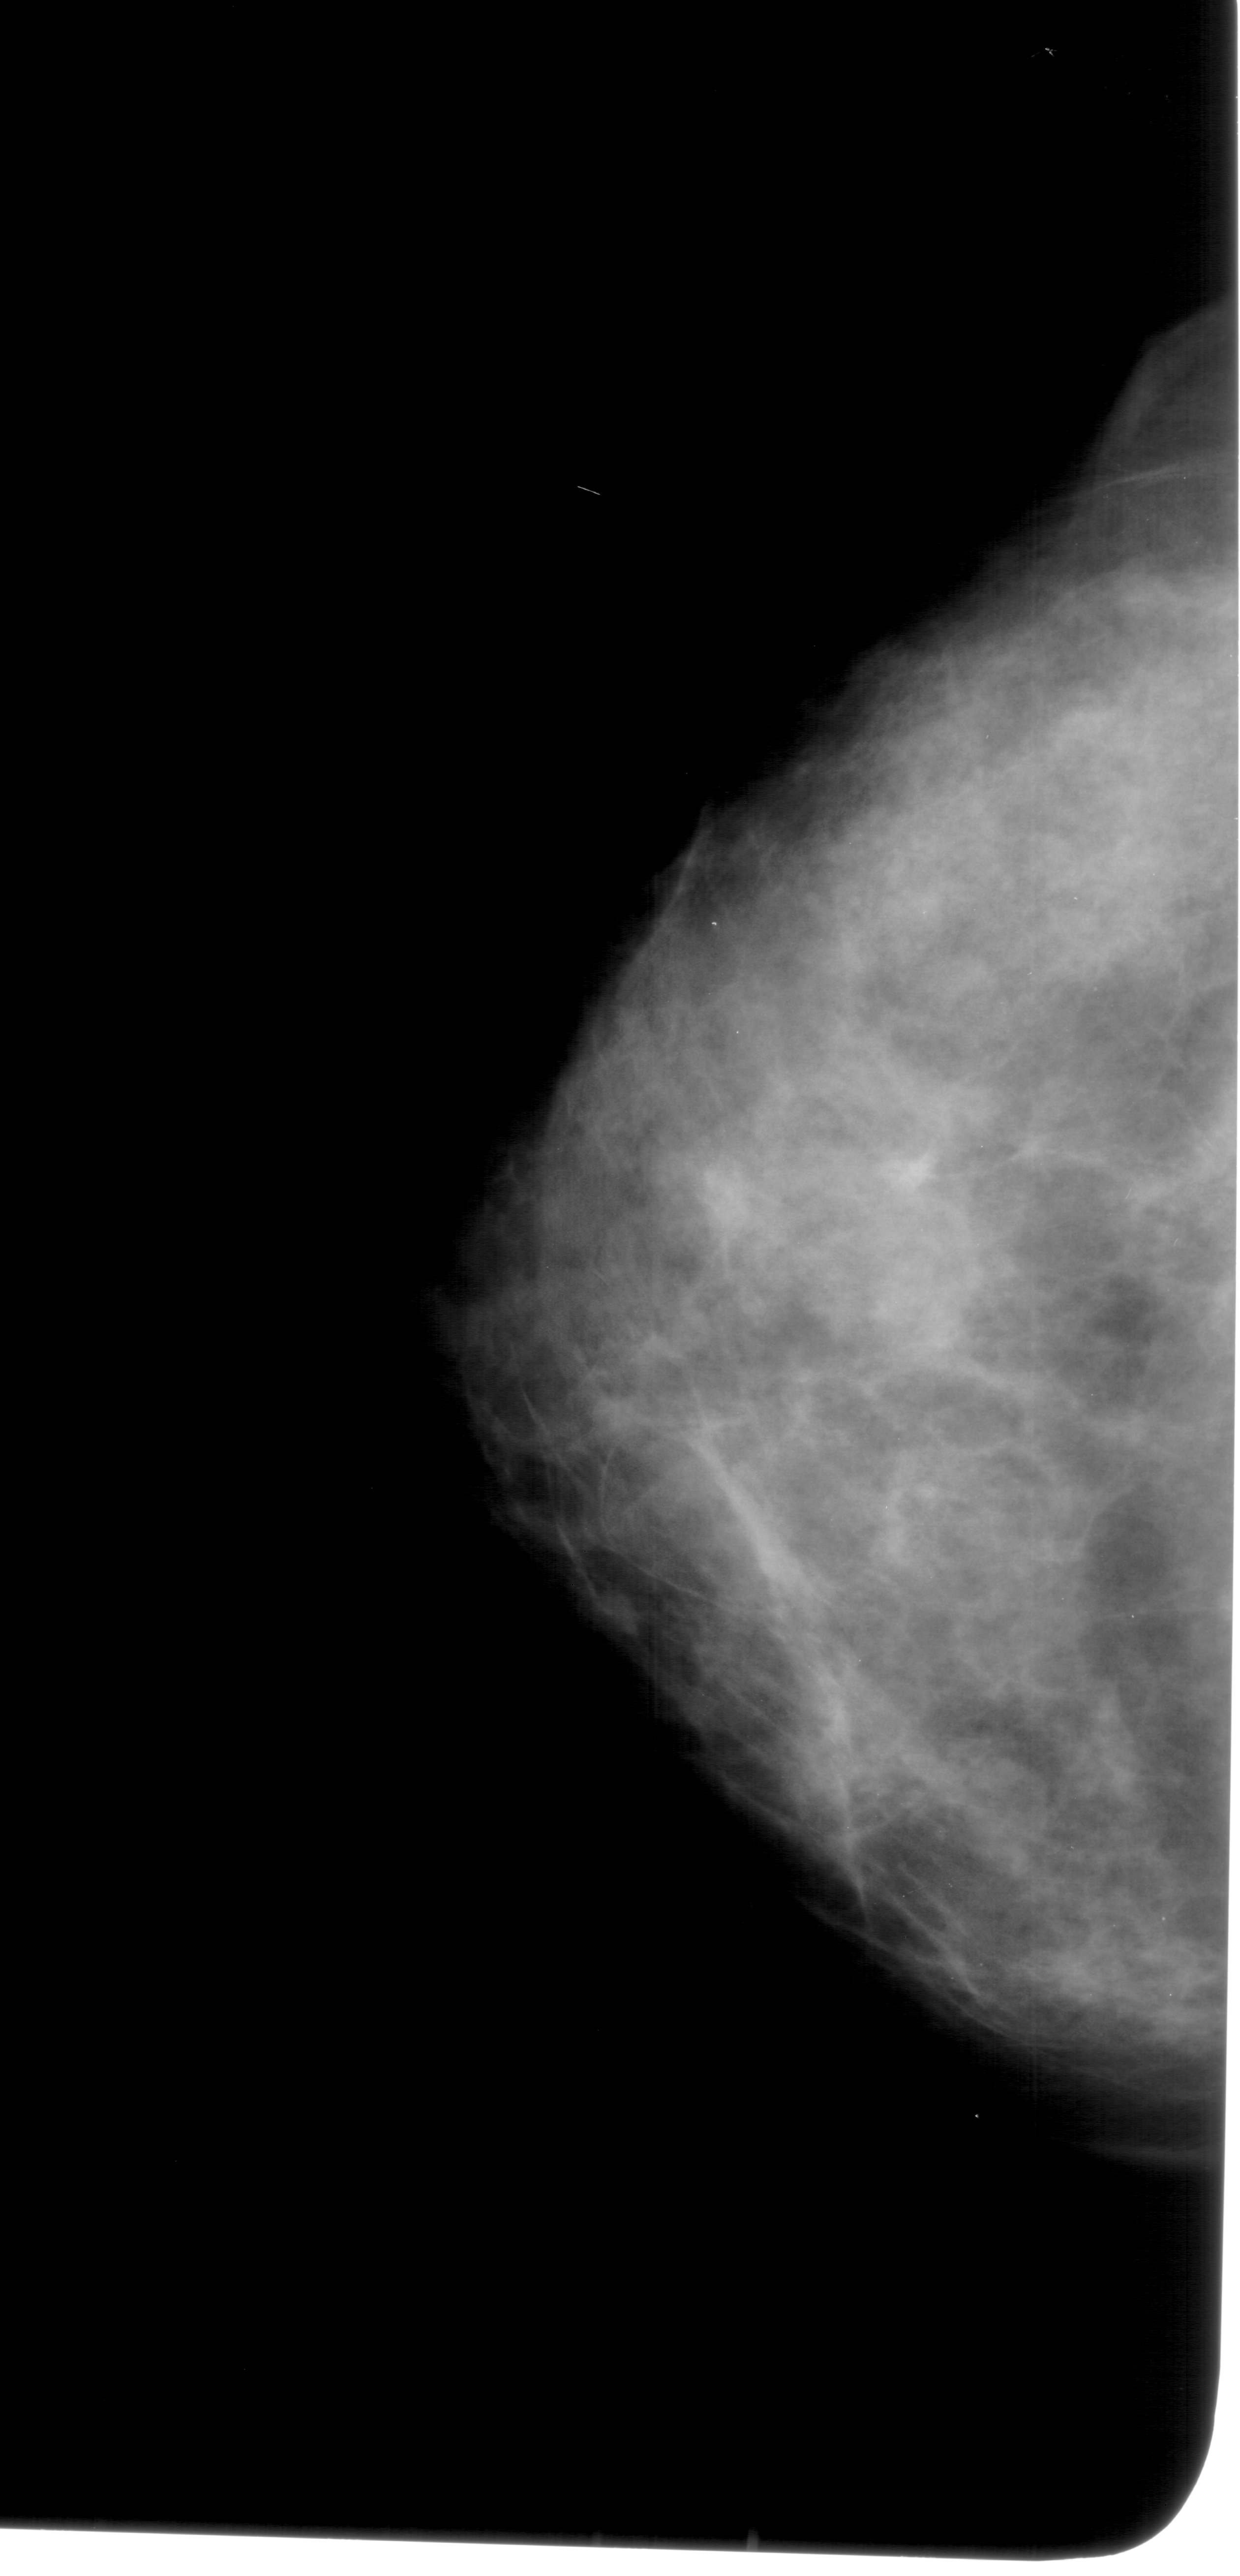
Digitized screen-film mammogram; left breast; craniocaudal (CC) view; BI-RADS breast density category 4 (scale 1–4); 1240 × 2576 image matrix.
Expert-marked regions of interest on this film, with their recorded descriptors:
- mass, shape round, margins circumscribed; BI-RADS assessment category 4; subtlety rating 3 on a 1 (subtle) to 5 (obvious) scale; pathology result (as recorded, not read from the image): benign: bounding box (x1, y1, x2, y2) in pixels: (939, 1745, 1059, 1862)